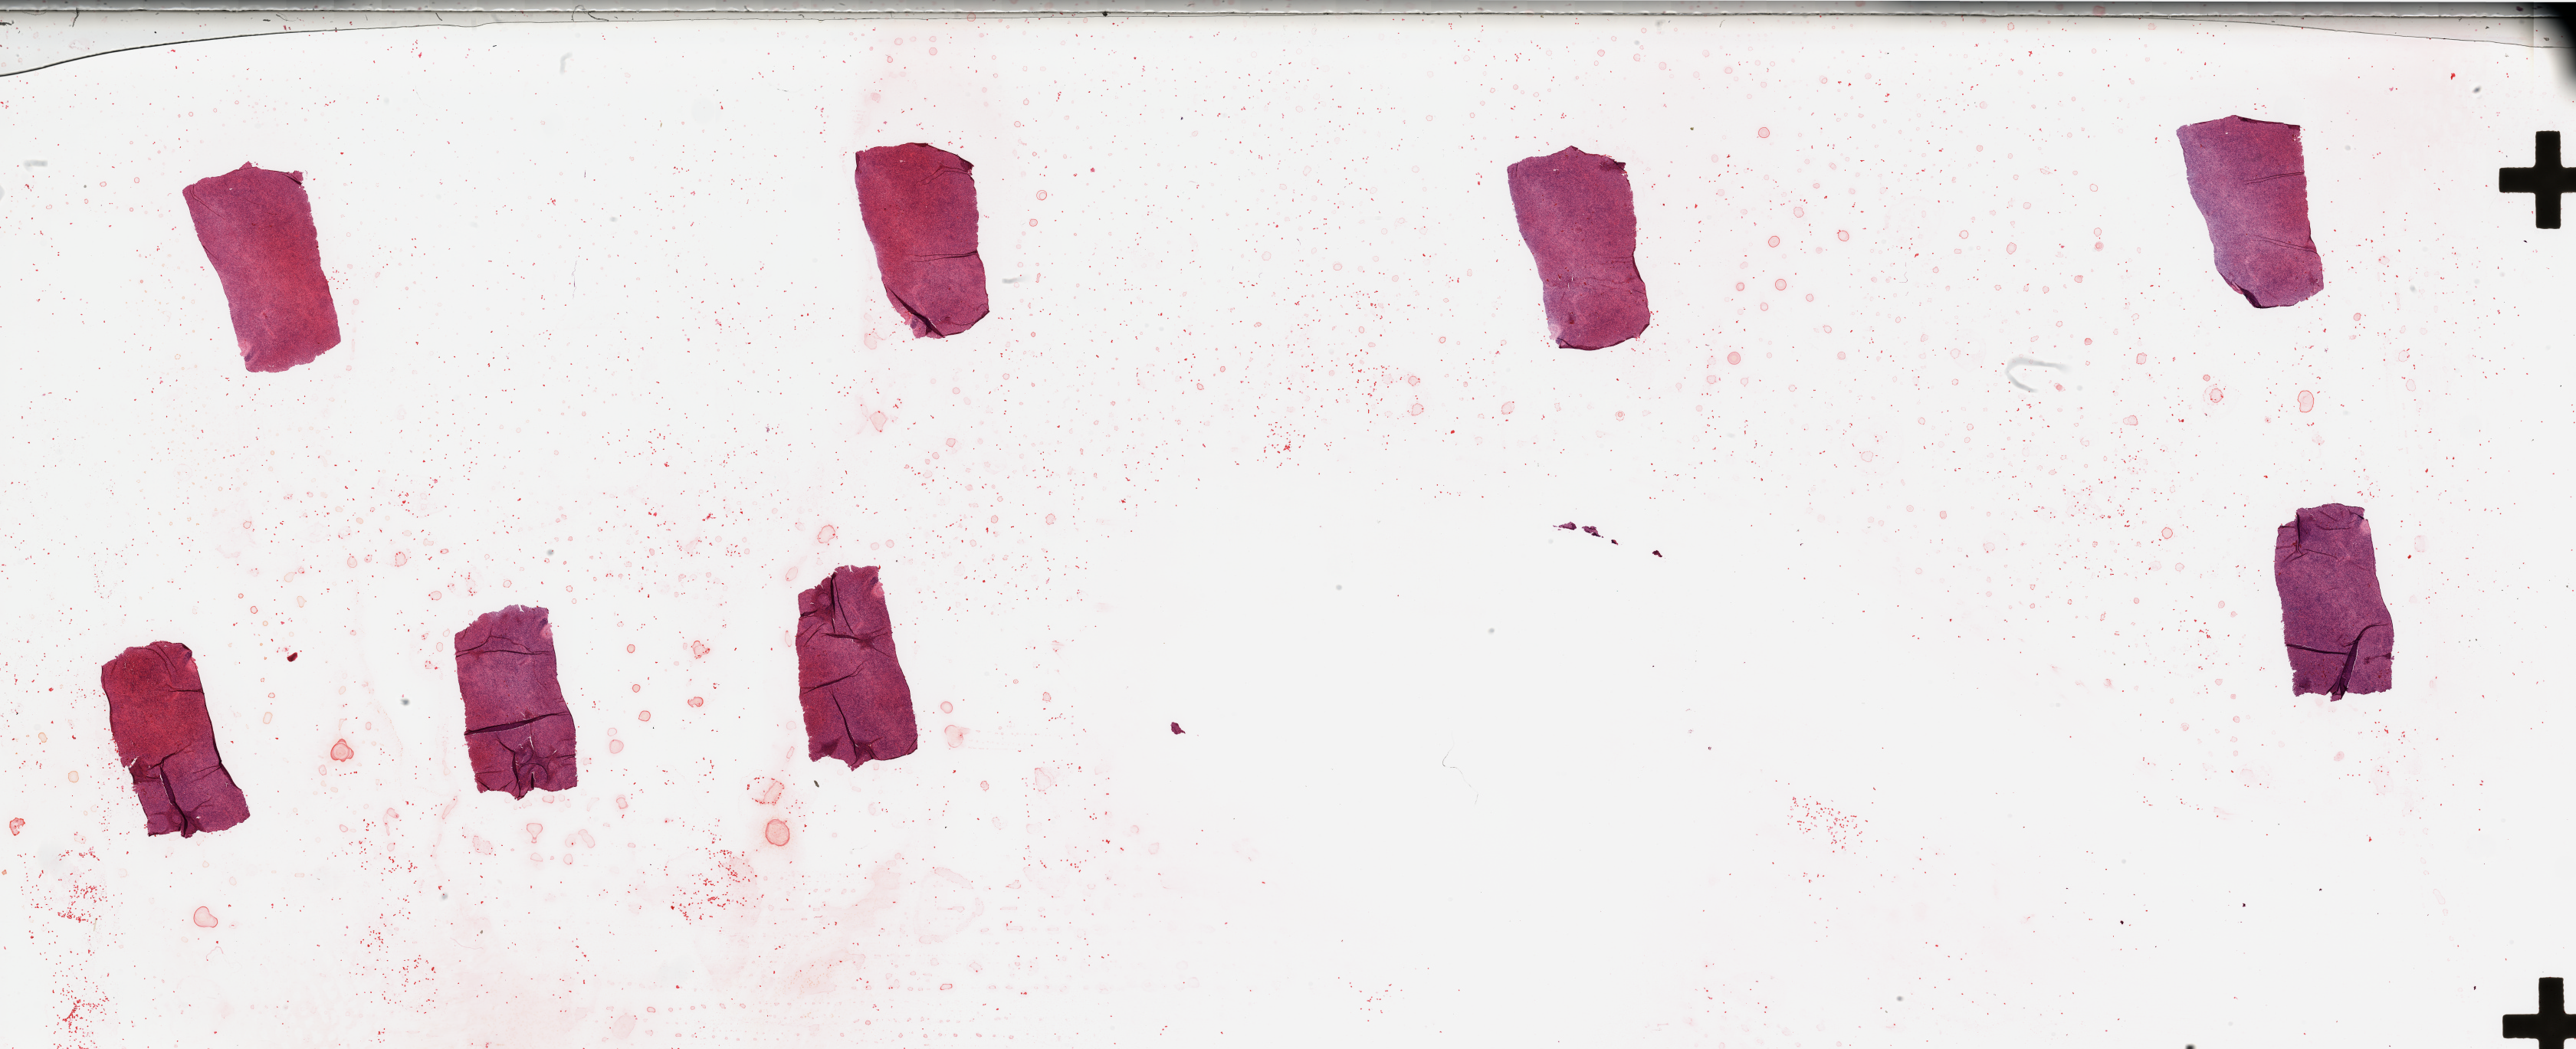
Digitized H&E-stained tissue section (whole slide), whole scanned area (about 53.2 x 21.7 mm, from a 20x scan) shown as a low-resolution overview; tumour tissue sample. 75-year-old female patient.
Patient diagnosis (cohort enrolment): sarcoma (site not recorded at cohort level).